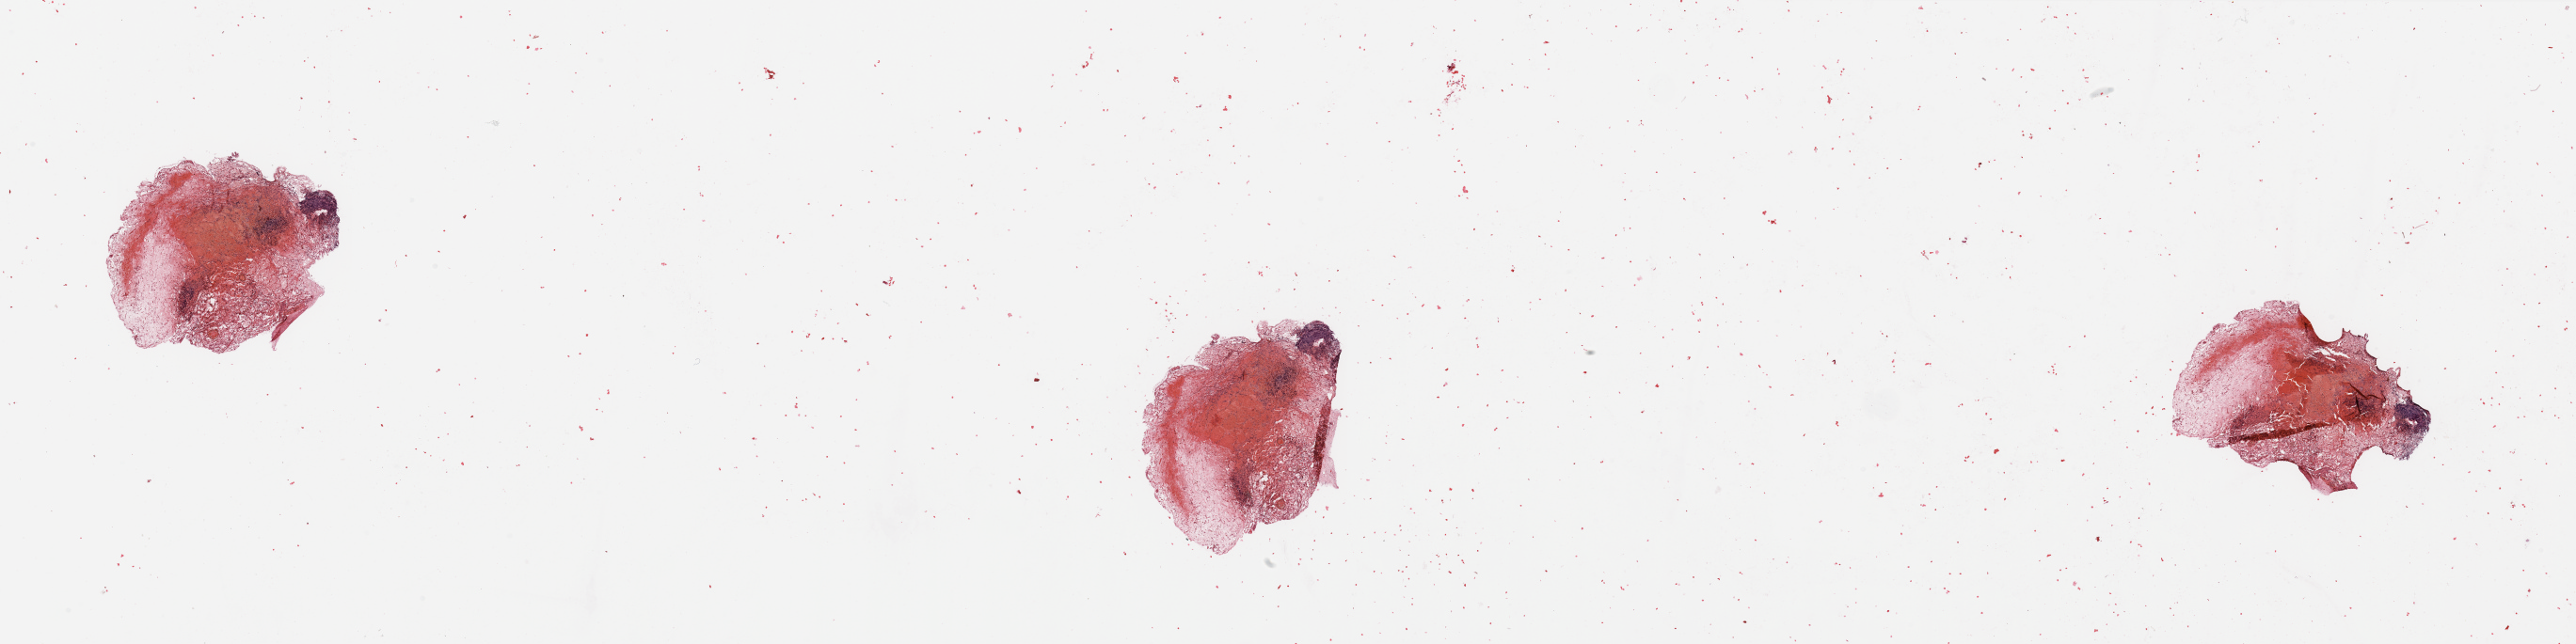
Whole-slide histology image, H&E — a low-resolution overview of the entire scanned area, about 43.3 x 10.8 mm (acquisition: 20x scan). Kidney, tumour tissue. Patient: male, age 74 years. Histologic grade: G1 (well differentiated).
AJCC pathologic stage: I. Primary tumour site (as recorded): middle. Histologic diagnosis: Renal cell carcinoma, NOS.